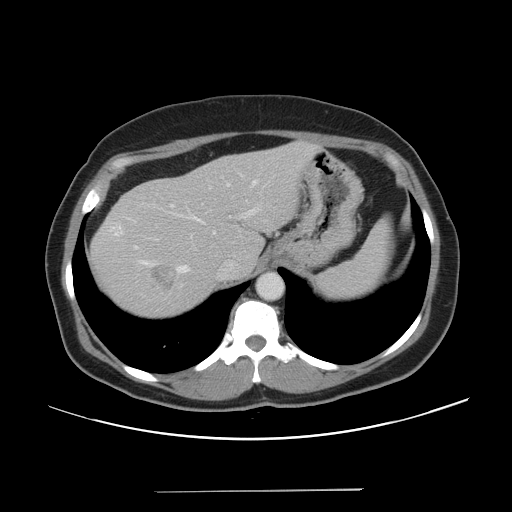
Contrast-enhanced abdominal CT, one axial slice; position 36 of 56 along the scan axis; 120 kVp; intravenous contrast given; soft-tissue window (W 400 / L 40 HU); 5 mm slice thickness; 512 × 512 image matrix, field of view 419 × 419 mm. Female patient, age 54 years. From the clinical record (not read from this slice): diagnosis: colorectal cancer liver metastases, imaged before liver resection; multiple liver metastases: yes; largest metastasis: 3.2 cm; disease in both lobes: yes.
Structures marked on this image (outlined manually by an expert reader):
- hepatic veins: bounding box (x1, y1, x2, y2) in pixels: (133, 179, 259, 274)
- liver: (90, 142, 318, 317)
- planned liver remnant (the part of the liver to remain after resection): (190, 141, 318, 272)
- portal vein (with intrahepatic branches): (209, 182, 231, 190)
- liver metastasis: (152, 265, 175, 290)
- liver metastasis: (112, 220, 124, 235)